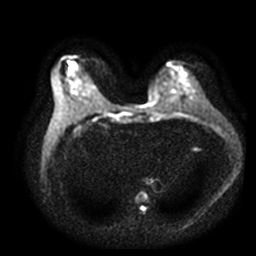
Breast MRI, one axial slice; diffusion-weighted series; image 2 of 4 stored at this slice position (different b-values; order by instance number); 3 T; 256 × 256 image matrix, field of view 360 × 360 mm. Female patient.
Outlined on this slice (expert manual segmentation):
- tumour on diffusion-weighted imaging: bounding box [x1, y1, x2, y2] px = [69, 67, 73, 74]